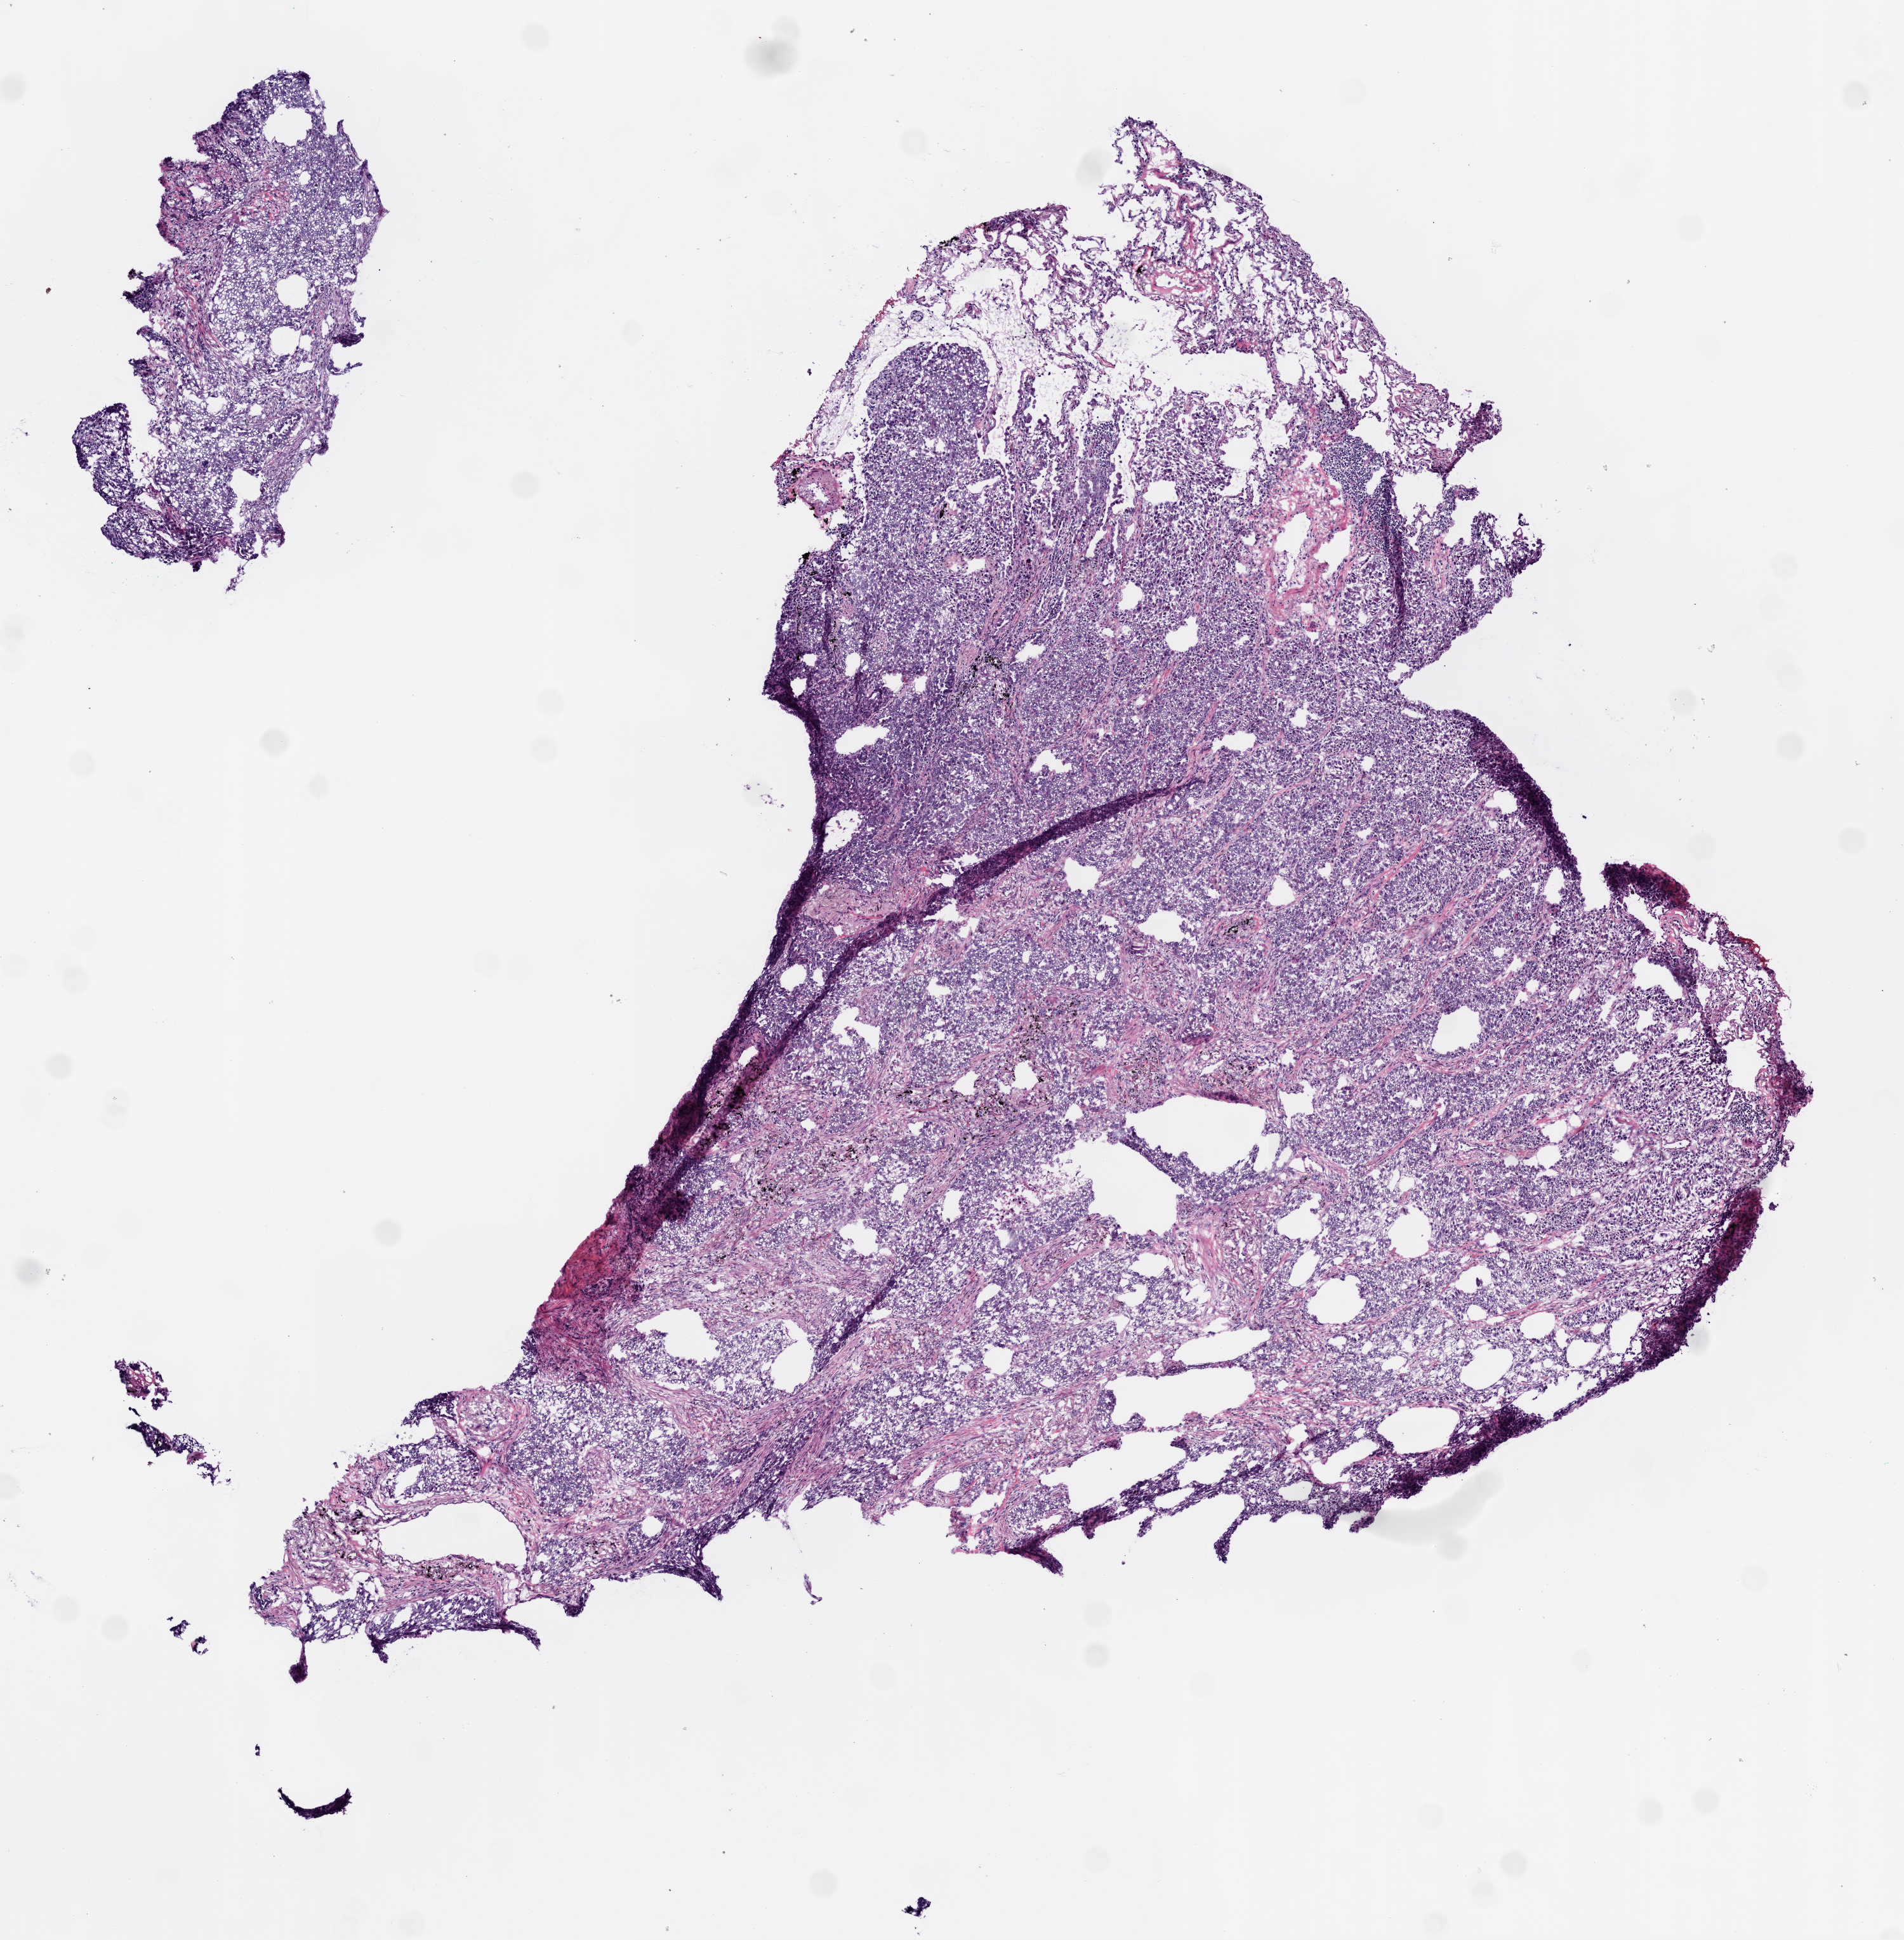
Whole-slide histology image, Hematoxylin and eosin (H&E) stained — a low-resolution overview of the entire scanned area, about 6.0 x 6.1 mm. Frozen section from the top of the tissue portion. Primary tumour sample from the lung. Female, age 74 years at initial diagnosis. Slide review estimates, as recorded: tumour cells 90%, tumour nuclei 90%, normal cells 5%, stromal cells 5%, necrosis 0%.
TNM: T1 N0 M0. Histologic diagnosis: Clear cell adenocarcinoma, NOS (lower lobe, lung). AJCC pathologic stage: IA (6th edition).